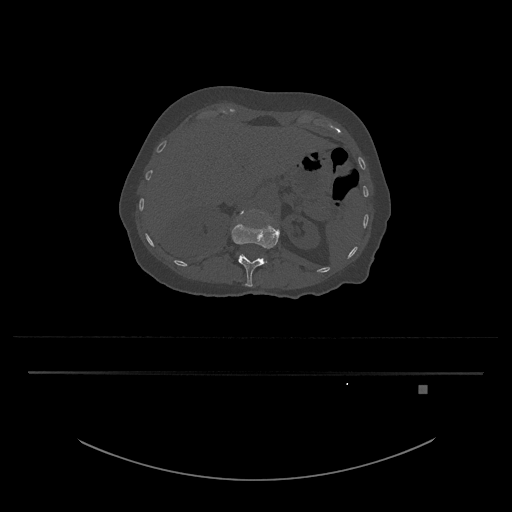
CT including the spine, one axial slice. Slice 540 of 797 in the series (ordered by position). Reconstruction kernel Br40s/3. 120 kVp. Bone window (W 1800 / L 400 HU). 512 × 512 image matrix. Female patient, age 57 years. Case-level facts recorded for this patient, not image findings: primary cancer: cervical.
Structures marked on this image (semi-automatic segmentation, software-assisted and operator-edited):
- L1 vertebra: bounding box (x1, y1, x2, y2) in pixels: (231, 218, 280, 287)